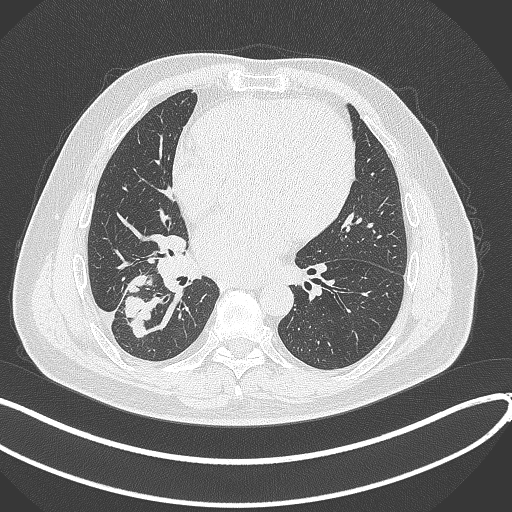
Chest CT, one axial slice. Position 164 of 360 along the scan axis. Reconstruction kernel B70f. Lung window (W 1500 / L -600 HU). 1 mm slice thickness. 512 × 512 image matrix, field of view 400 × 400 mm. Male patient, age 59 years.
Structures marked on this image (bounding box drawn by a radiologist):
- lung tumour (recorded histology: adenocarcinoma): bounding box [x1, y1, x2, y2] px = [125, 270, 161, 339]